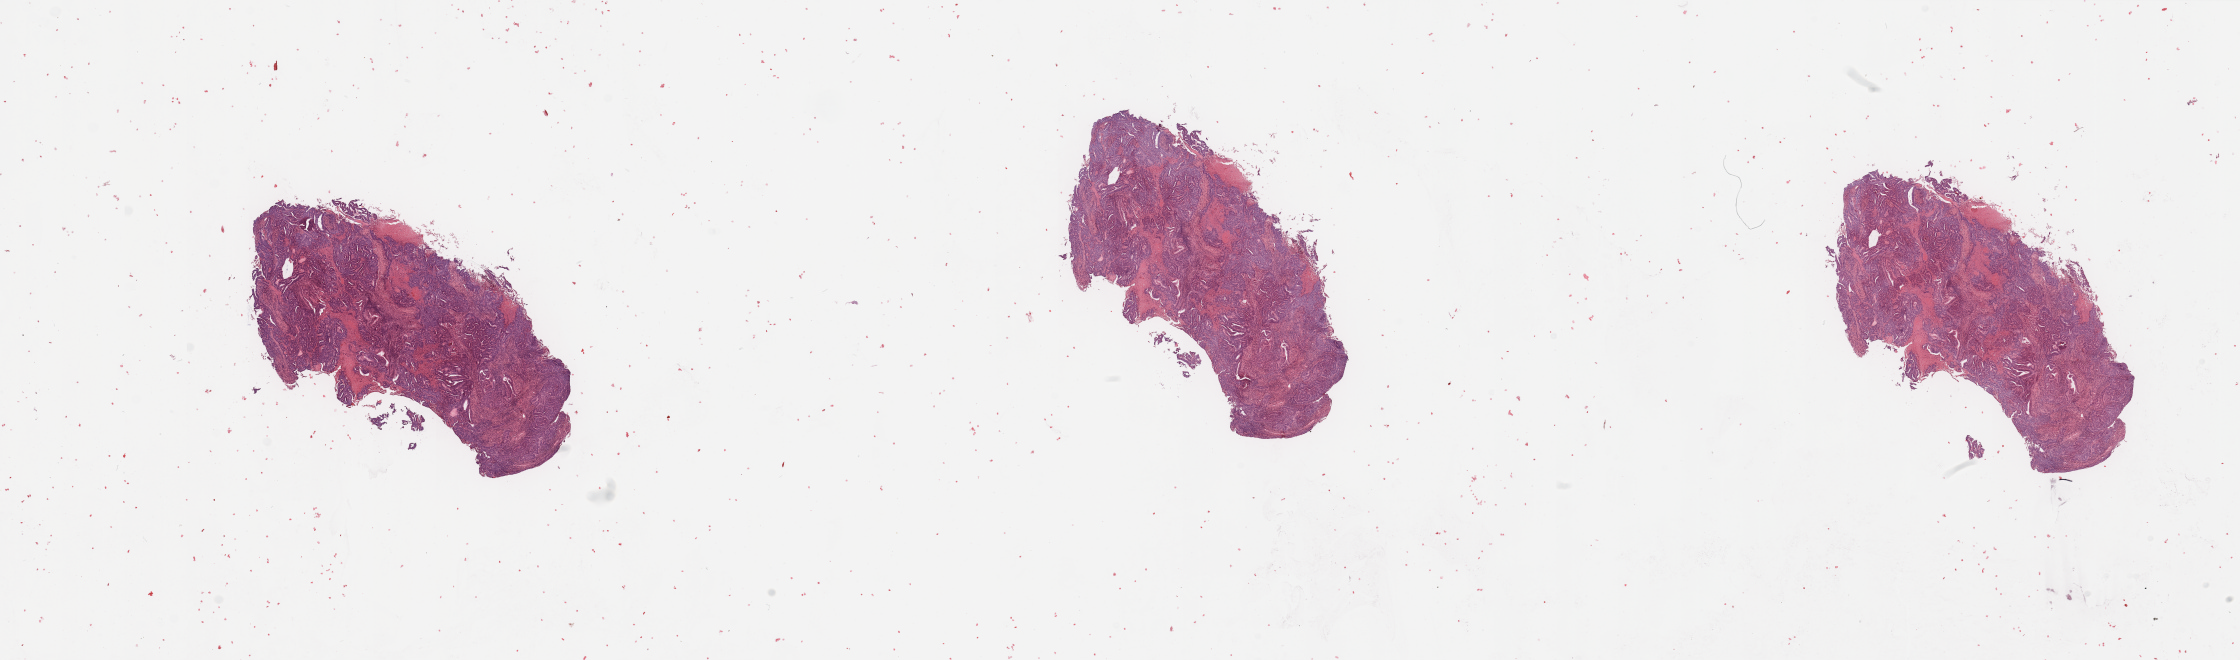
Whole-slide histology image, Hematoxylin and eosin (H&E) stained — a low-resolution overview of the entire scanned area, about 35.4 x 10.4 mm; tumour tissue sample, sampled site: uterus. Patient: female, age 58 years. Histologic grade: G2 (moderately differentiated). Slide review estimates, as recorded: tumour nuclei 80%, necrosis 20%.
* diagnosis: Endometrioid adenocarcinoma, NOS
* AJCC pathologic stage: III
* primary tumour site (as recorded): anterior endometrium